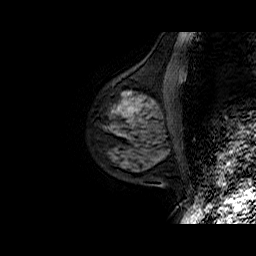
Breast MRI (dynamic contrast-enhanced), one sagittal slice; slice 20 of 50 in the series (ordered by position); dynamic contrast-enhanced series, time point 2 of 6 at this slice position (early post-contrast); 1.5 T; TE 6.5 ms, TR 32.9 ms; 4 mm slice thickness; 256 × 256 image matrix, field of view 200 × 200 mm. Female patient. From the clinical record (not read from this slice): setting: breast cancer imaged before/during neoadjuvant chemotherapy; receptor status: HR-positive, HER2-negative.
Annotated regions visible in this slice (semi-automatic segmentation, software-assisted and operator-edited):
- analysis volume of interest (the breast-tissue region the enhancement analysis was run in; not a lesion): bounding box (x1, y1, x2, y2) in pixels: (103, 75, 178, 149)
- tumour enhancement mask (voxels above the 100 % enhancement threshold inside the analysis volume of interest): (117, 108, 130, 110)